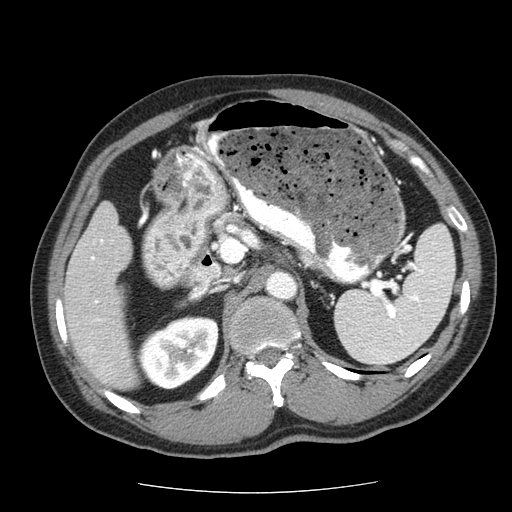
Contrast-enhanced abdominal CT (liver protocol), one axial slice; slice 25 of 85 in the series (ordered by position); reconstruction kernel STANDARD; soft-tissue window (W 400 / L 40 HU); 2.5 mm slice thickness; 512 × 512 image matrix, field of view 360 × 360 mm. From the clinical record (not read from this slice): diagnosis: hepatocellular carcinoma (patient treated with transarterial chemoembolisation; whether this scan precedes or follows treatment is not stated here); TNM stage (as recorded): Stage-IIIA; Child-Pugh class: A; tumour differentiation: well differentiated; tumour size: 8 cm.
Structures marked on this image (semi-automatic segmentation, software-assisted and operator-edited):
- liver parenchyma outside the tumour (the mass and vessels are separate outlines, so this box may not span the whole liver): box from (x=64, y=202) to (x=138, y=390) px
- liver vessels: (x=91, y=239)–(x=103, y=351)